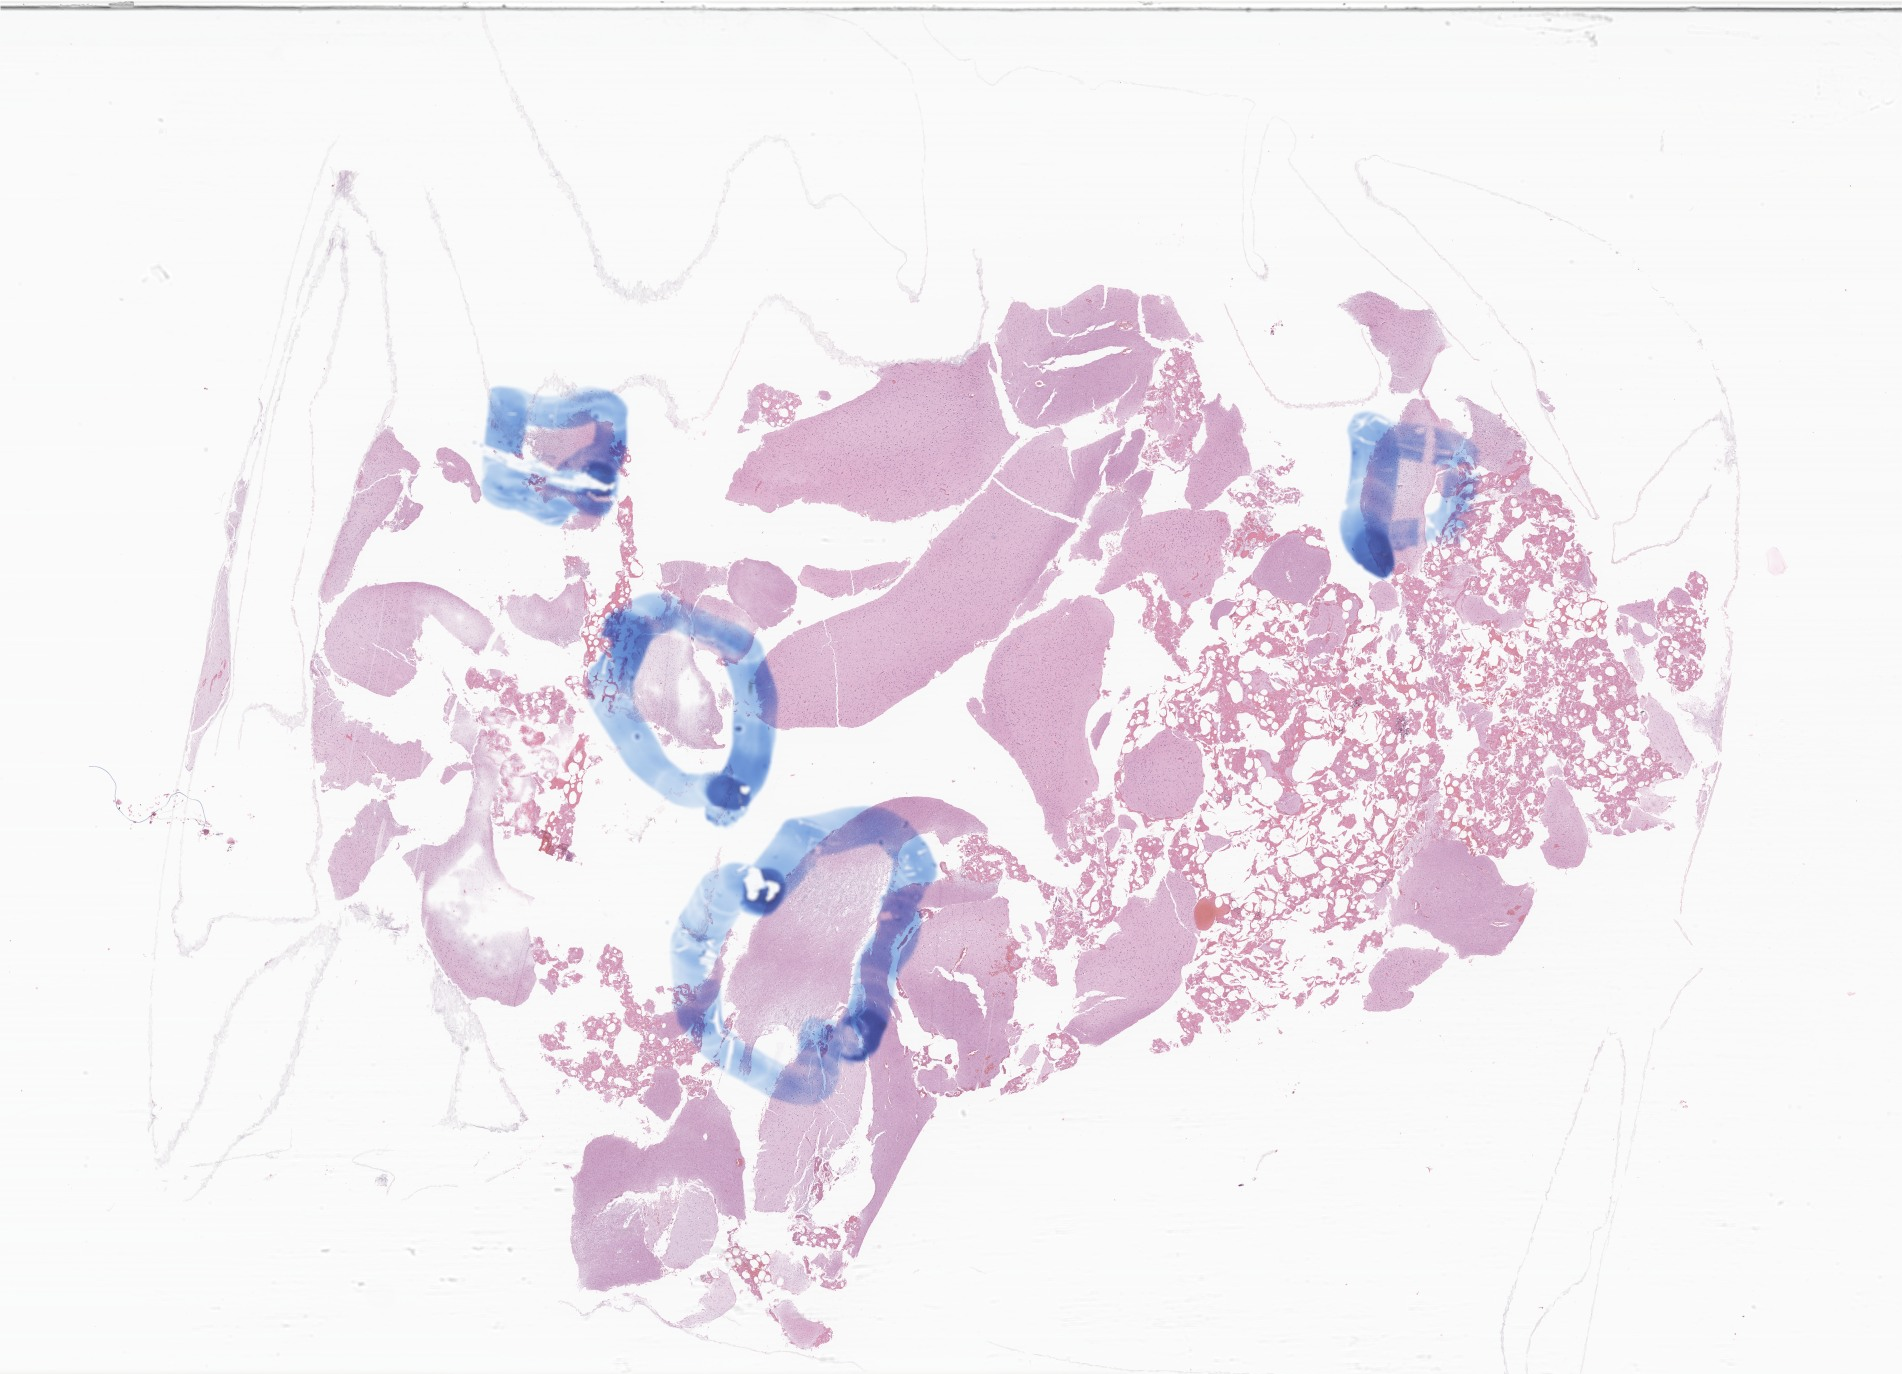
Digitized haematoxylin and eosin-stained section of tumor tissue from the frontal lobe, a low-resolution overview of the entire scanned area, about 32.1 x 23.2 mm; formalin-fixed paraffin-embedded section. Patient: male, age 203 months.
- diagnosis: Neoplasm, uncertain whether benign or malignant